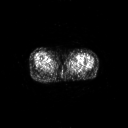
FDG PET of an extremity soft-tissue mass (from a PET/CT study), one axial slice. Slice 57 of 91 in the series (ordered by position). 128 × 128 image matrix, field of view 700 × 700 mm. Female patient, age 74 years. From the clinical record (not read from this slice): histological type: pleomorphic leiomyosarcoma; grade: high; site of the primary tumour: left thigh.
Structures marked on this image (expert contour drawn on MRI and transferred to this co-registered scan by the dataset authors):
- gross tumour volume including surrounding oedema: bounding box (x1, y1, x2, y2) in pixels: (68, 55, 72, 59)